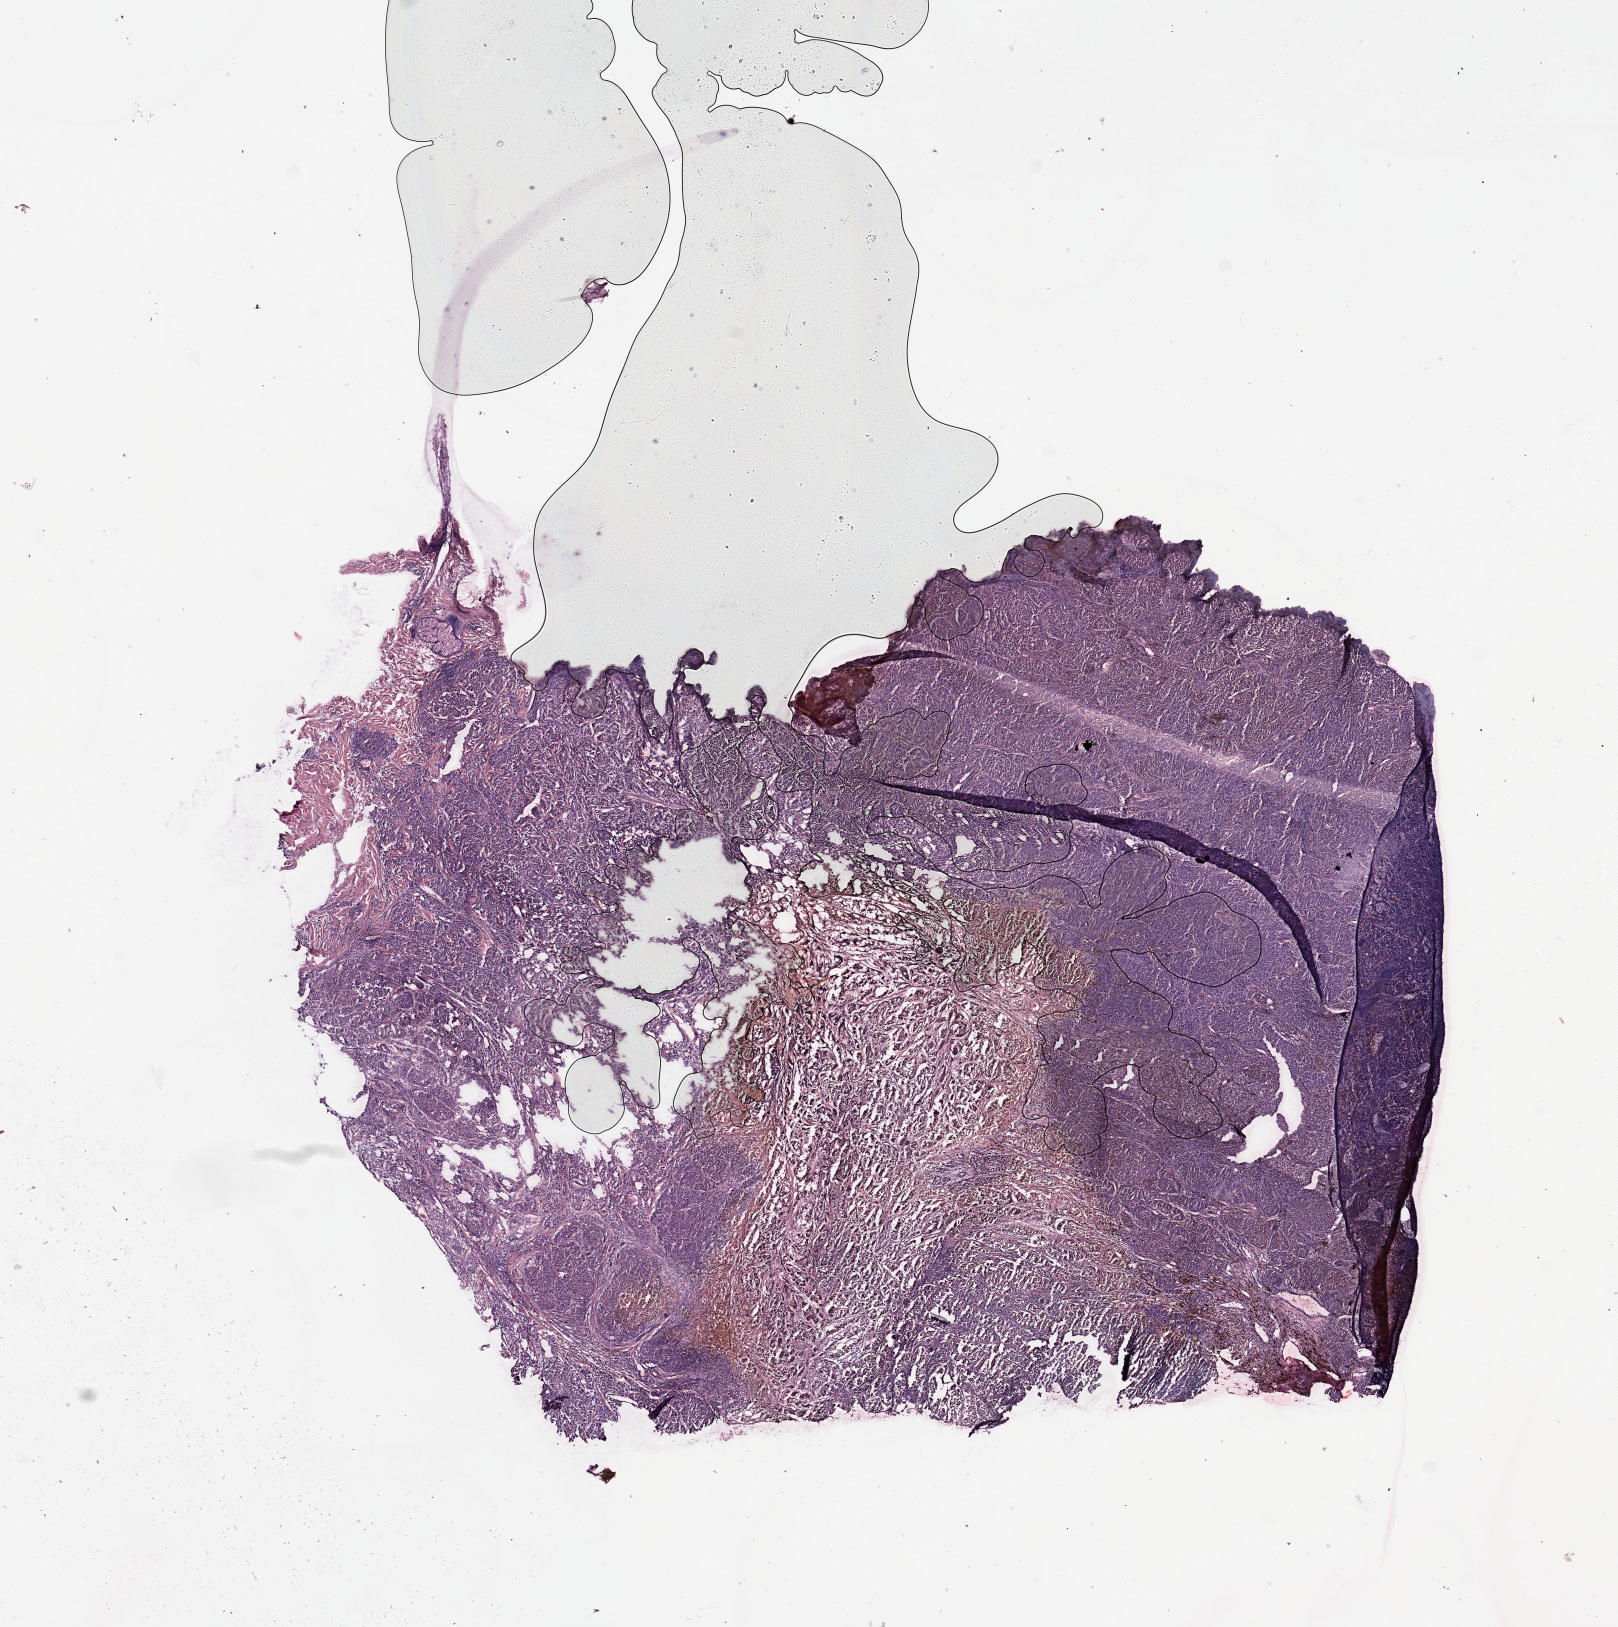
Whole-slide histology image, H&E-stained, low-resolution overview of the scanned area, about 12.8 x 12.9 mm (from a 20x scan); melanoma tumour tissue; sampled site not recorded. Male, 54 y/o.
- primary tumour site (as recorded): trunk
- patient diagnosis (cohort enrolment): cutaneous melanoma (skin)